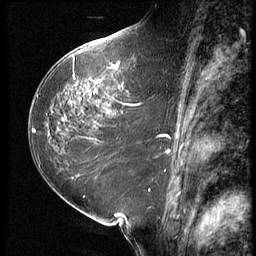
Breast MRI (dynamic contrast-enhanced), one sagittal slice; position 33 of 64 along the scan axis; 3 images stored at this slice position (order not interpretable as contrast timing); 1.5 T; TE 4.2 ms, TR 9 ms; 2.5 mm slice thickness; 256 × 256 image matrix. Female patient, age 59 years. Case-level facts recorded for this patient, not image findings: setting: breast cancer imaged before/during neoadjuvant chemotherapy; receptor status: HER2-positive.
Annotated regions visible in this slice (semi-automatic segmentation, software-assisted and operator-edited):
- analysis volume of interest (the breast-tissue region the enhancement analysis was run in; not a lesion): bounding box [x1, y1, x2, y2] px = [54, 65, 155, 132]
- tumour enhancement mask (voxels above the 140 % enhancement threshold inside the analysis volume of interest): [63, 65, 140, 121]